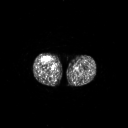
FDG PET of an extremity soft-tissue mass (from a PET/CT study), one axial slice. Slice 253 of 311 in the series (ordered by position). 3.27 mm slice thickness. 128 × 128 image matrix. Patient: male, 56 years. Case-level facts recorded for this patient, not image findings: histological type: pleiomorphic leiomyosarcoma; grade: intermediate; site of the primary tumour: right thigh.
Structures marked on this image (expert contour drawn on MRI and transferred to this co-registered scan by the dataset authors):
- gross tumour volume including surrounding oedema: bounding box <43,56,51,62> (left, top, right, bottom; pixels)